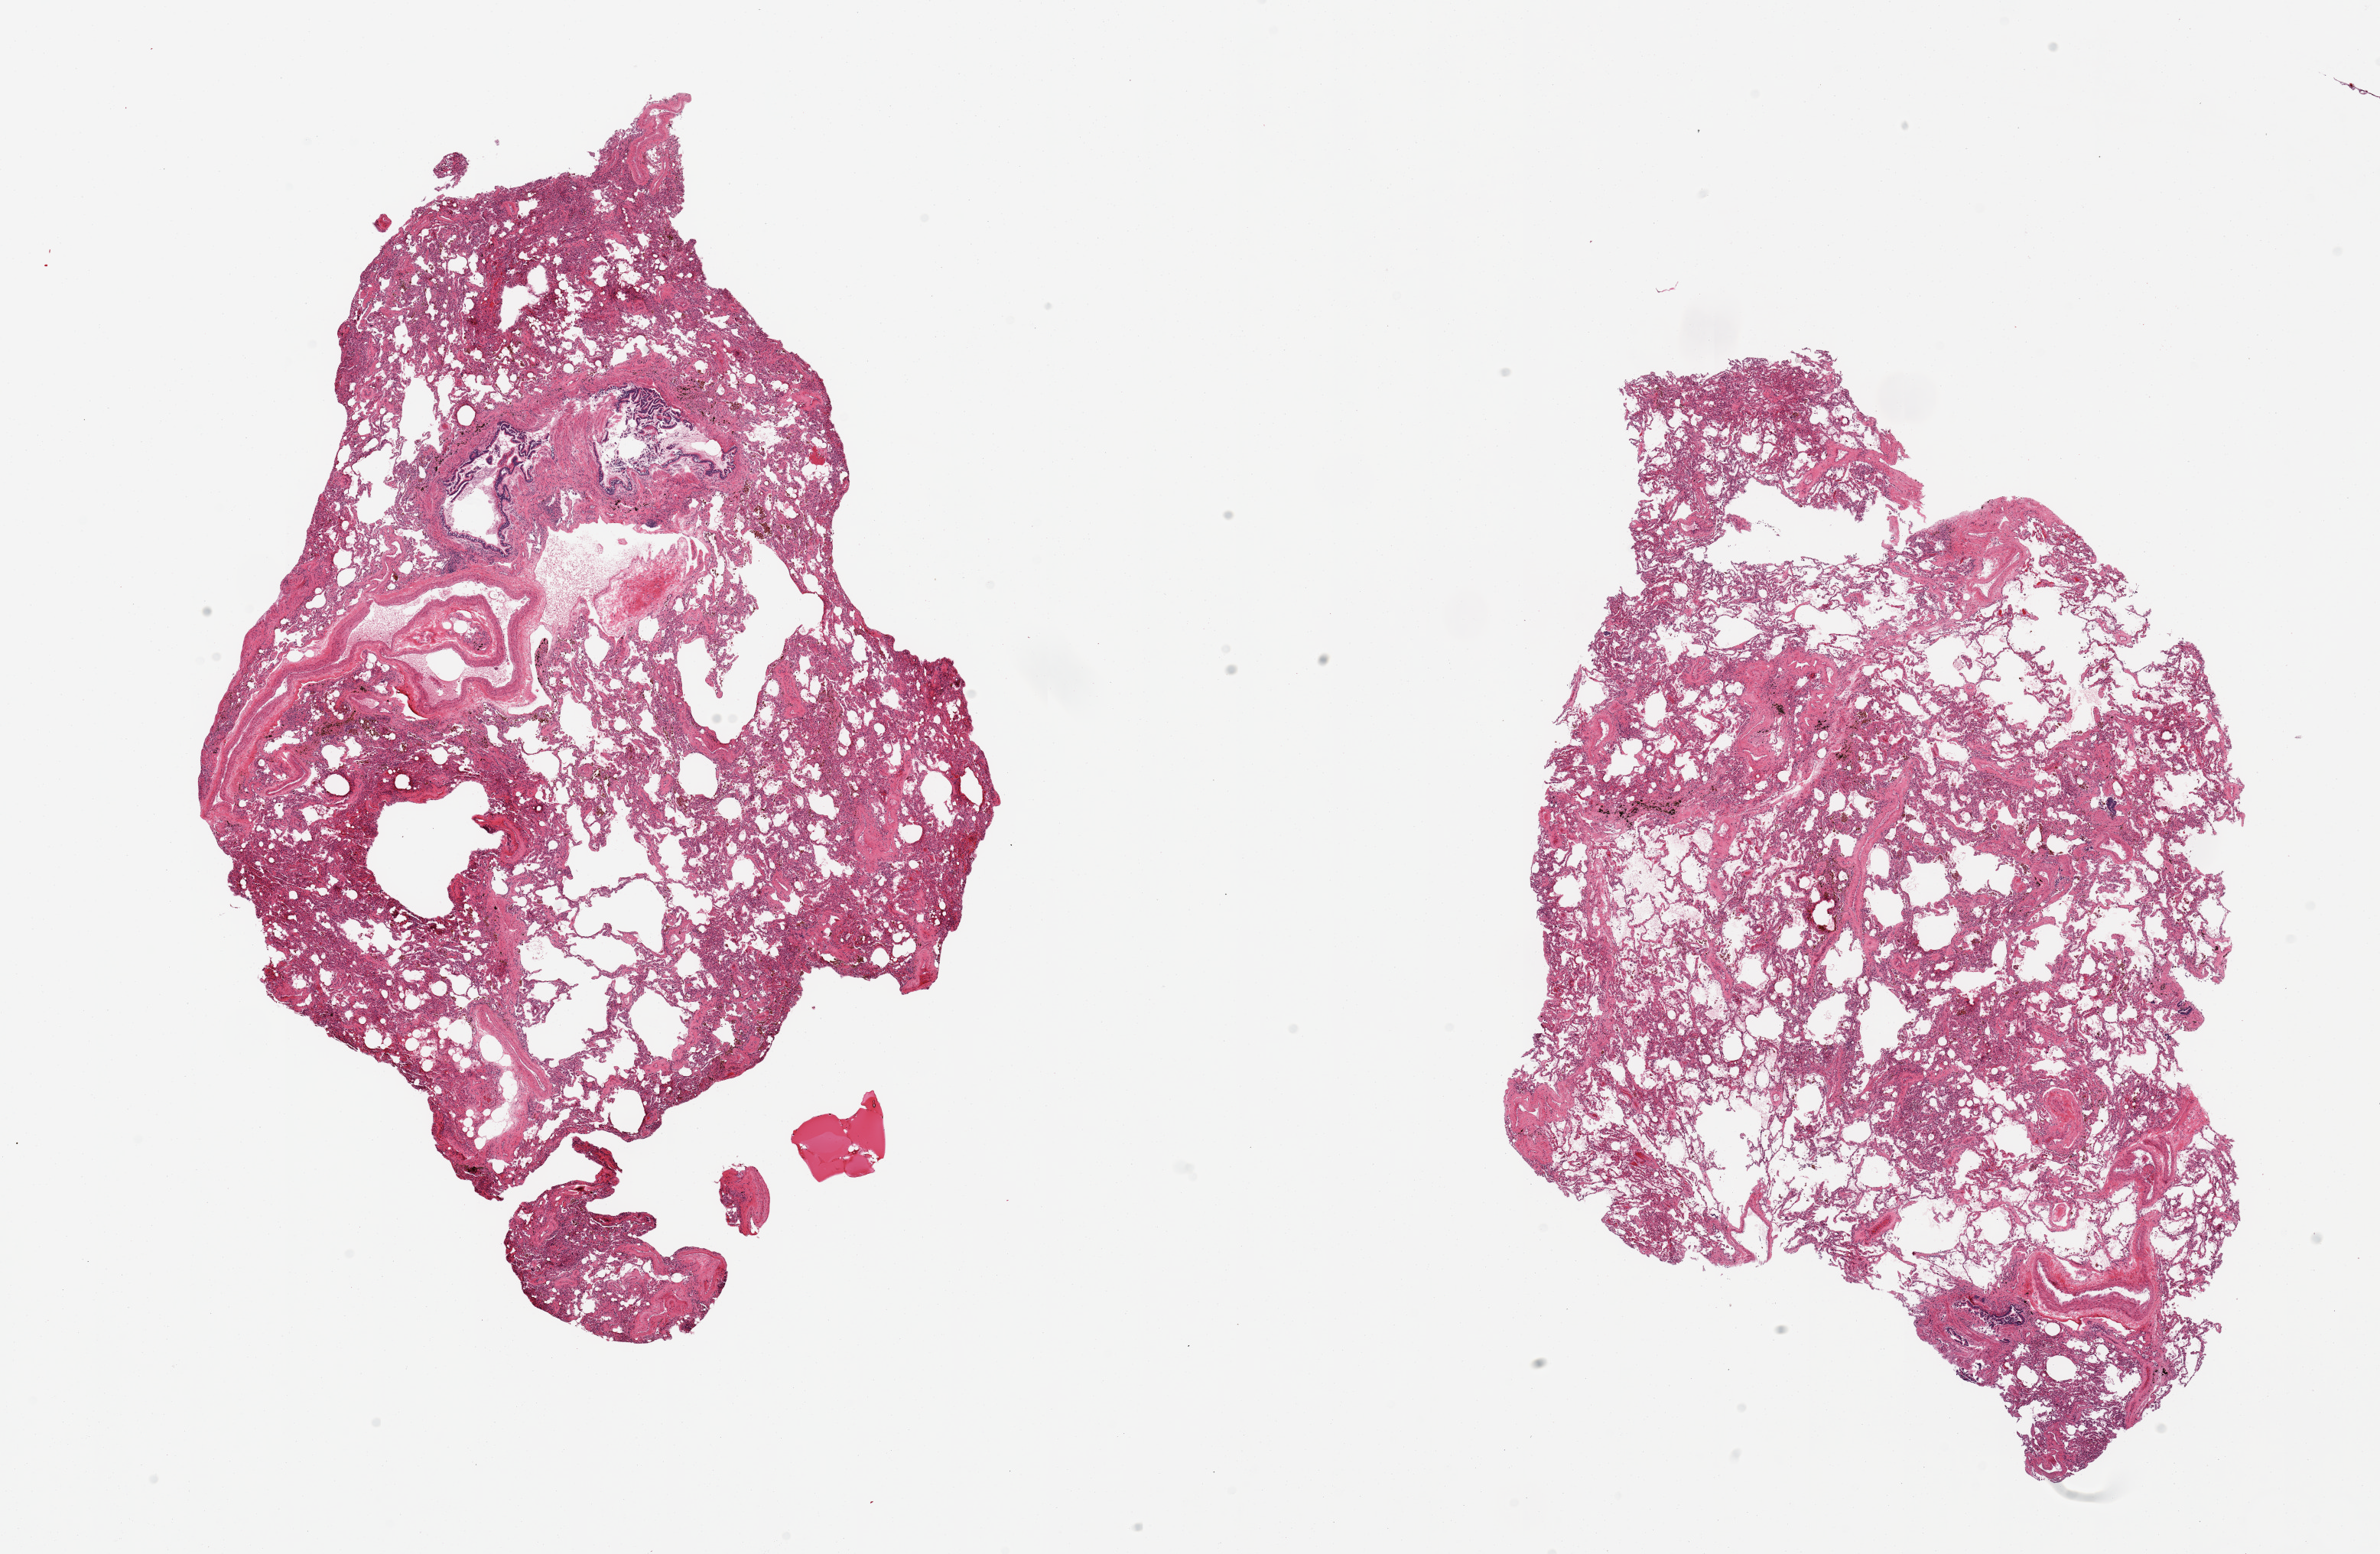
Digitized H&E-stained section, brightfield, low-resolution overview of the scanned area, about 24.6 x 16.1 mm. PAXgene-fixed paraffin-embedded (PFPE) section. Target tissue: lung. Tissue donor sample. Male donor.
Review note (as recorded): 2 pieces, emphysematous changes, marked congestive changes, fibrosis.